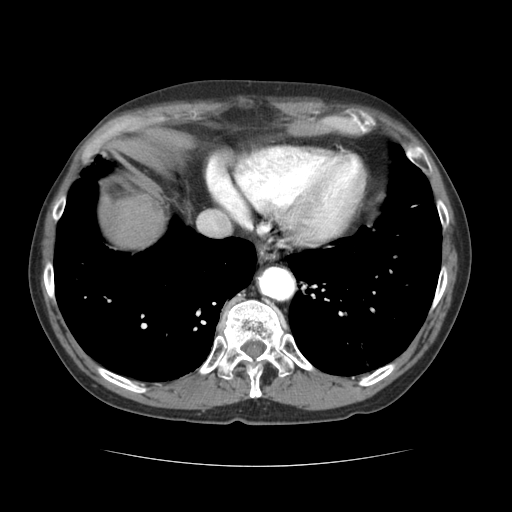
Contrast-enhanced abdominal CT (liver protocol), one axial slice; position 60 of 69 along the scan axis; reconstruction kernel STANDARD; 120 kVp; soft-tissue window (W 400 / L 40 HU); 2.5 mm slice thickness; 512 × 512 image matrix. Case-level facts recorded for this patient, not image findings: diagnosis: hepatocellular carcinoma (patient treated with transarterial chemoembolisation; whether this scan precedes or follows treatment is not stated here); TNM stage (as recorded): Stage-II; Child-Pugh class: B; tumour differentiation: poorly differentiated; tumour size: 2.6 cm.
Annotated regions visible in this slice (semi-automatic segmentation, software-assisted and operator-edited):
- liver parenchyma outside the tumour (the mass and vessels are separate outlines, so this box may not span the whole liver): bounding box [x1, y1, x2, y2] px = [102, 196, 164, 248]